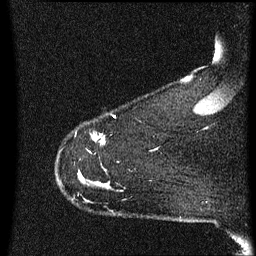
Breast MRI (dynamic contrast-enhanced), one sagittal slice. Slice 54 of 60 in the series (ordered by position). Dynamic contrast-enhanced series, image 2 of 3 at this slice position (ordered by acquisition). 1.5 T. TE 4.2 ms, TR 8.4 ms. 2 mm slice thickness. 256 × 256 image matrix, field of view 200 × 200 mm. Female patient, age 48 years.
Outlined on this slice (semi-automatic segmentation, software-assisted and operator-edited):
- analysis volume of interest (the breast-tissue region the enhancement analysis was run in; not a lesion): bounding box (x1, y1, x2, y2) in pixels: (78, 134, 111, 203)
- tumour enhancement mask (voxels above the 70 % enhancement threshold inside the analysis volume of interest): (93, 136, 105, 143)